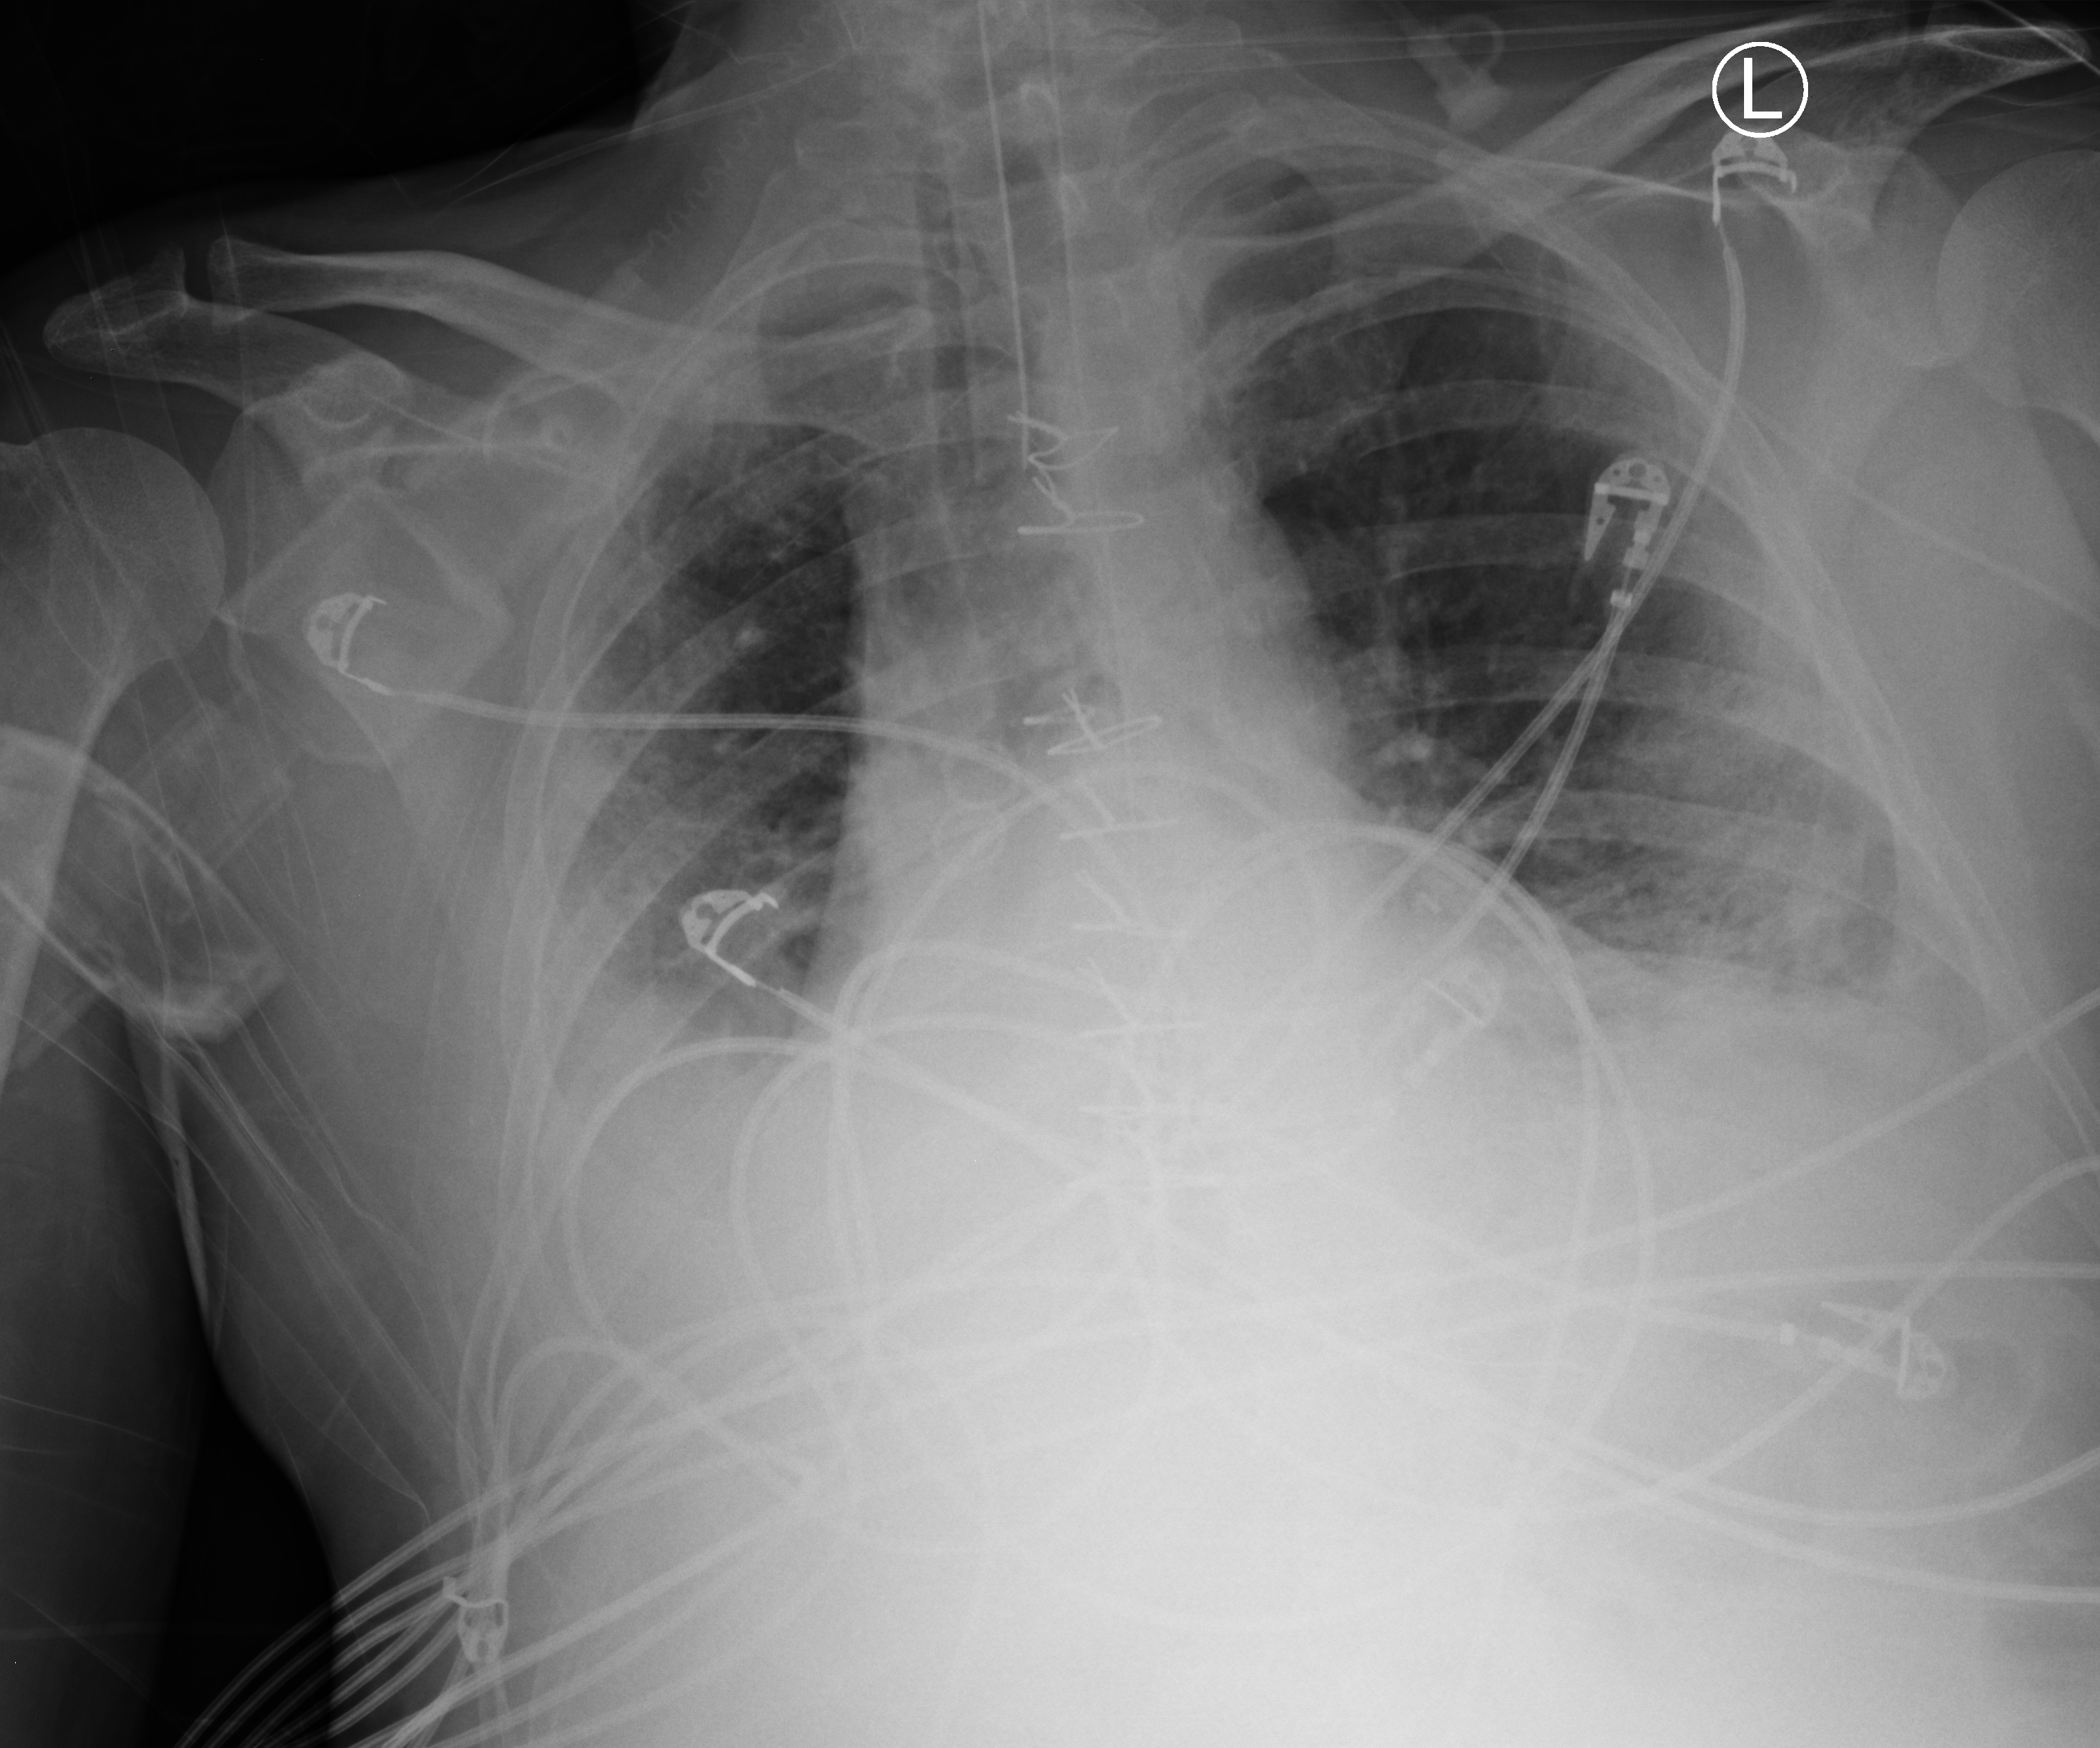
Portable chest radiograph, anteroposterior (AP) projection. Male patient hospitalised with COVID-19, age 18–59 years.
Admission-level facts for this patient (not findings on this image; timing relative to this image not recorded): mechanically ventilated during this hospital stay: yes.